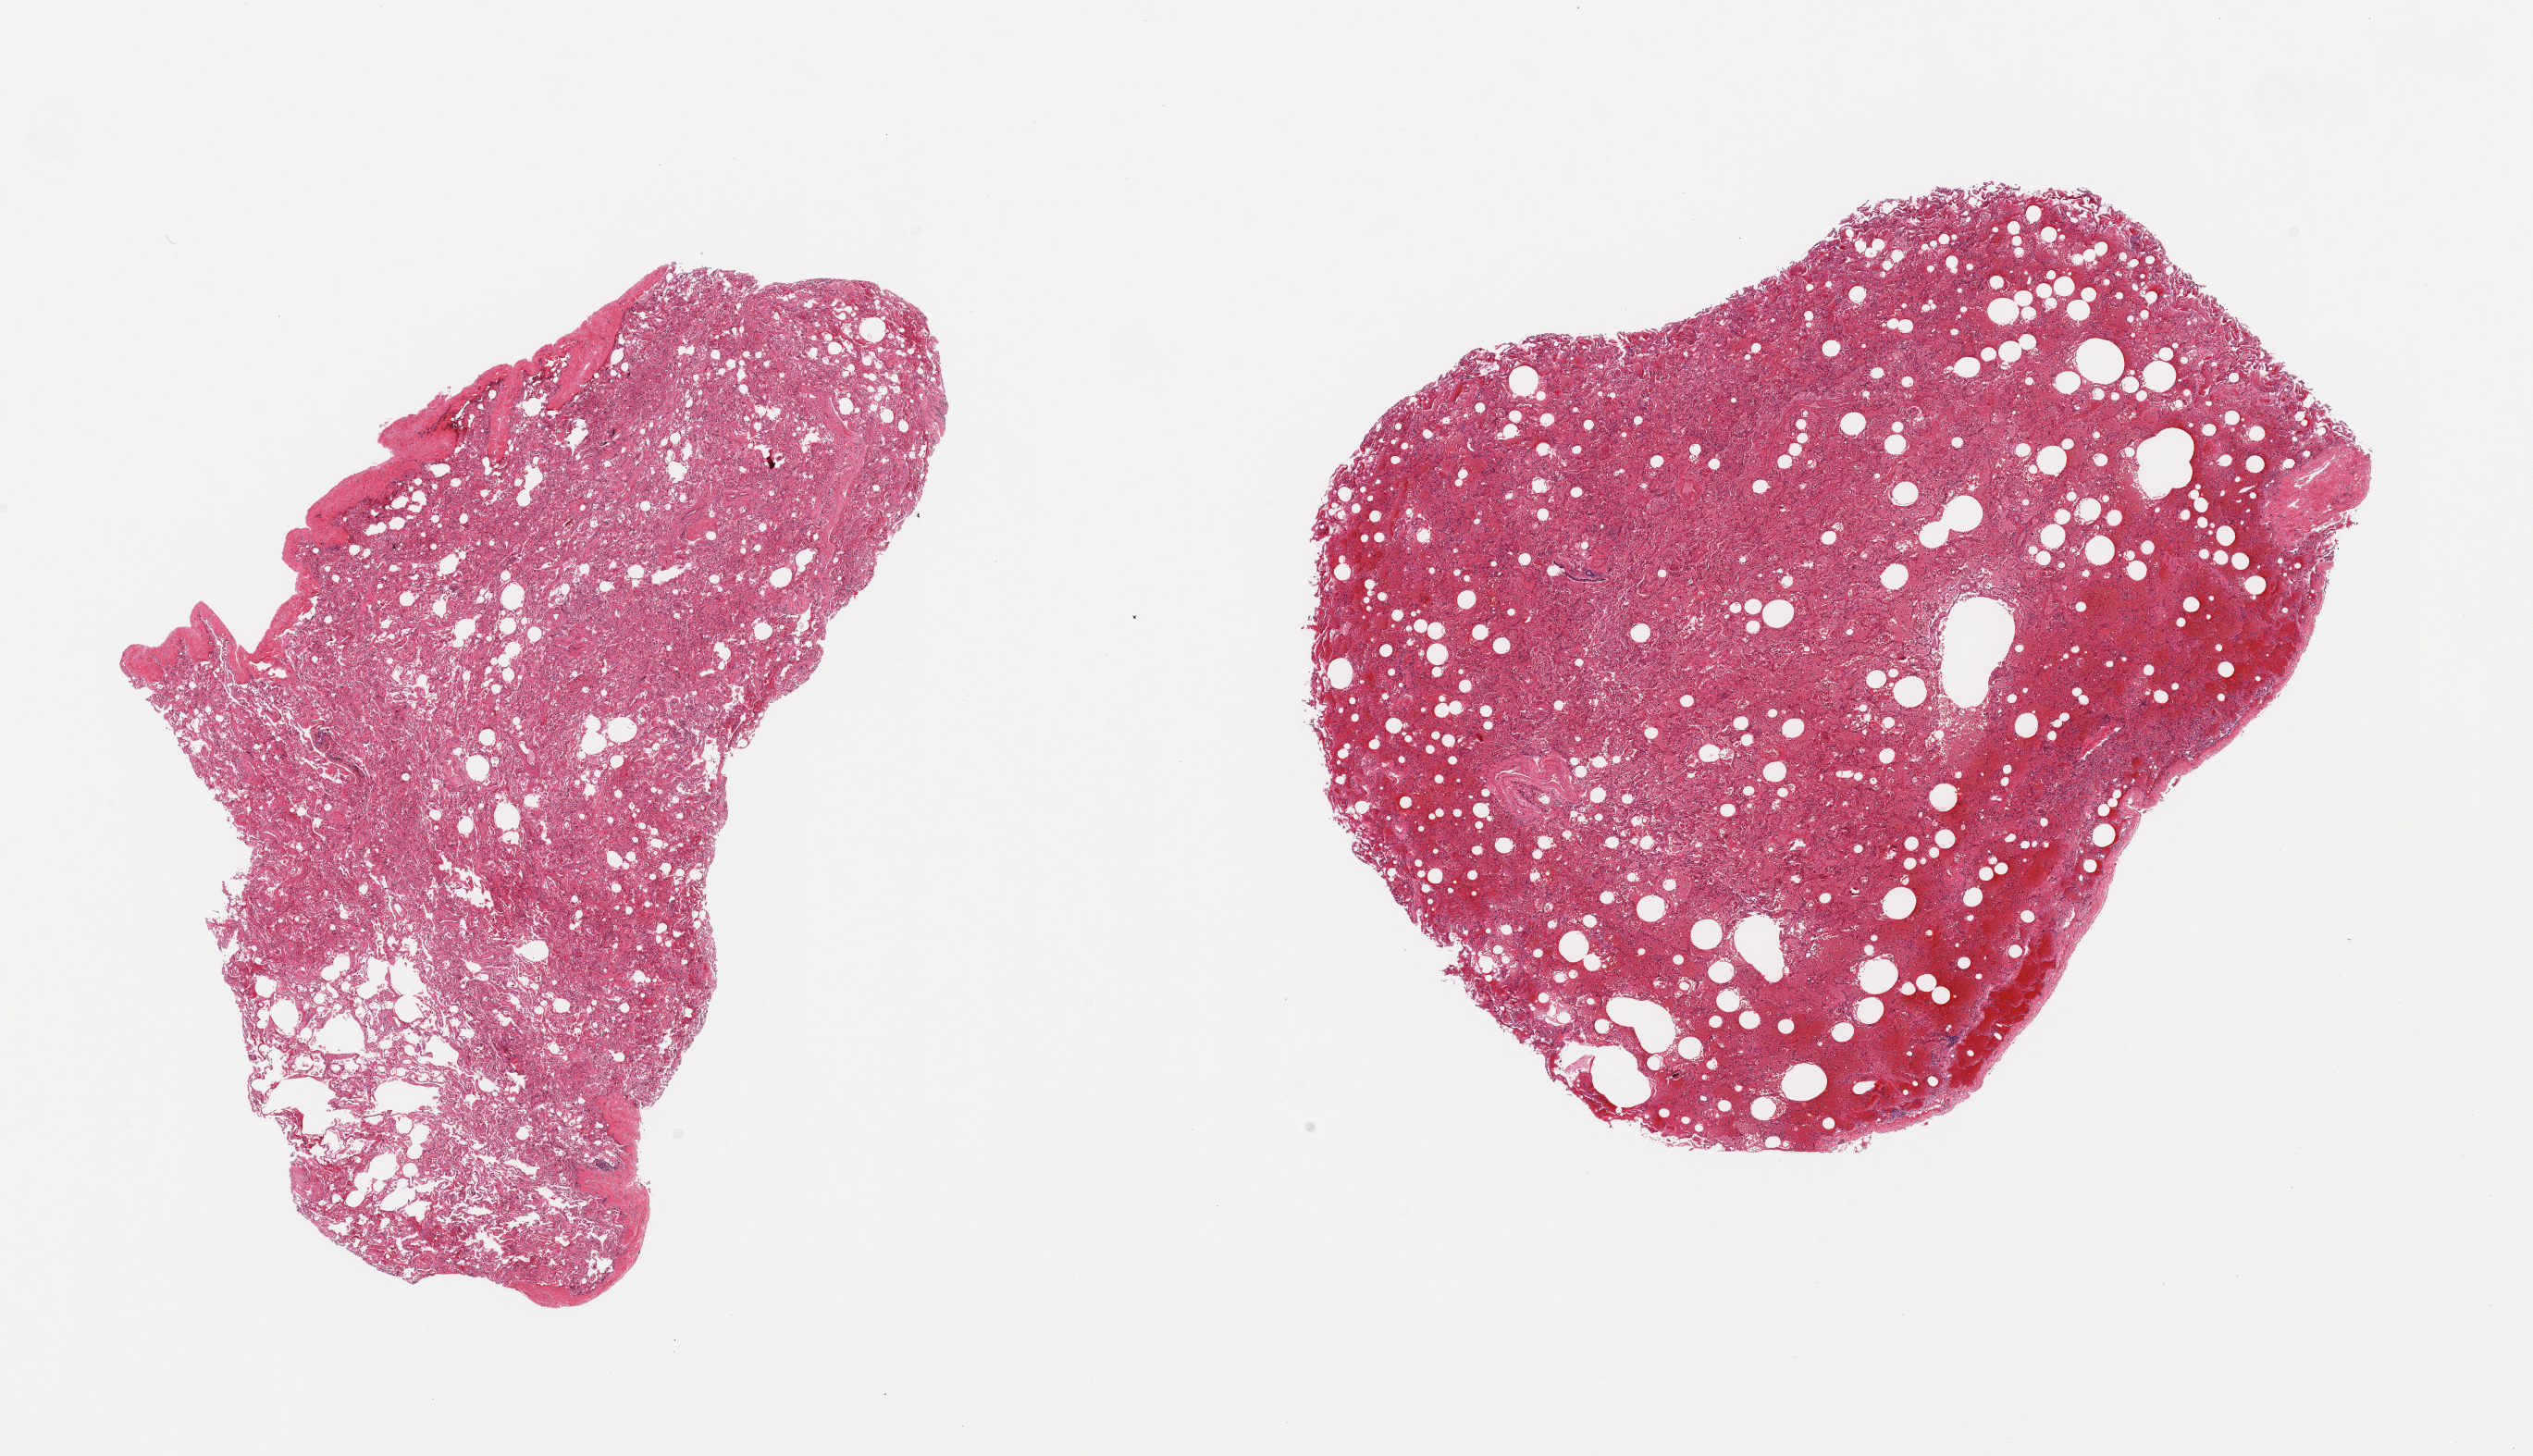
H&E whole-slide image, brightfield — low-resolution overview of the scanned area, about 21.7 x 12.5 mm, PAXgene-fixed, paraffin-embedded tissue, section of lung (target tissue), tissue donor sample. Donor sex: female.
- reviewer comment on this tissue sample: 2 pieces; extensive alveolar hemorrhage in 1; atelectasis in other; foci of emphysema